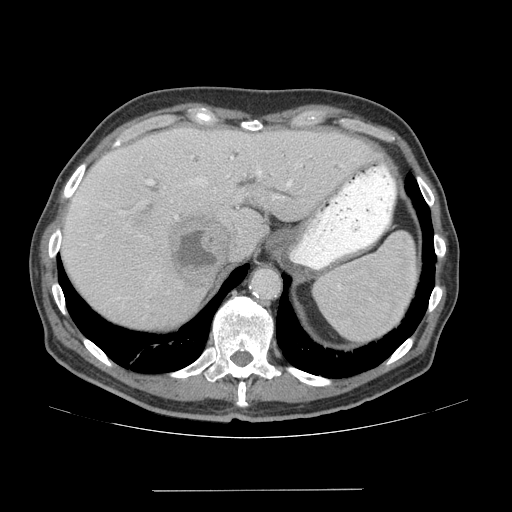
Contrast-enhanced abdominal CT (liver protocol), one axial slice. Slice 51 of 77 in the series (ordered by position). 140 kVp. Soft-tissue window (W 400 / L 40 HU). 2.5 mm slice thickness. 512 × 512 image matrix, field of view 400 × 400 mm. Case-level facts recorded for this patient, not image findings: diagnosis: hepatocellular carcinoma (patient treated with transarterial chemoembolisation; whether this scan precedes or follows treatment is not stated here); TNM stage (as recorded): Stage-IVA; Child-Pugh class: A; tumour differentiation: well differentiated; tumour nodularity: uninodular.
Annotated regions visible in this slice (semi-automatic segmentation, software-assisted and operator-edited):
- liver parenchyma outside the tumour (the mass and vessels are separate outlines, so this box may not span the whole liver): bounding box <60,126,372,328> (left, top, right, bottom; pixels)
- mass: <169,213,230,288>
- liver vessels: <74,140,343,237>